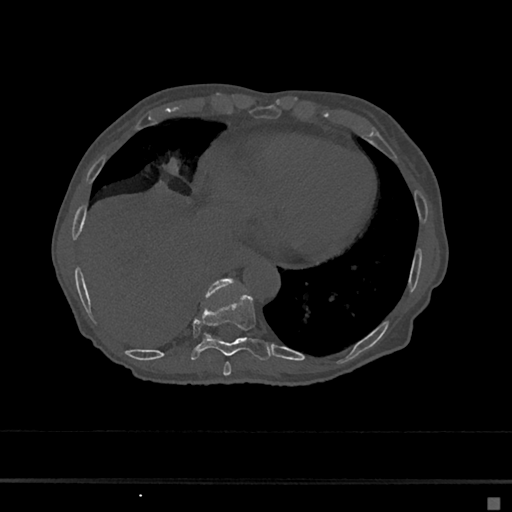
CT including the spine, one axial slice. Position 269 of 797 along the scan axis. 120 kVp. Bone window (W 1800 / L 400 HU). 512 × 512 image matrix, field of view 360 × 360 mm. Patient: female, 68 years. Case-level facts recorded for this patient, not image findings: primary cancer: renal.
Structures marked on this image (semi-automatic segmentation, software-assisted and operator-edited):
- T10 vertebra: box from (x=206, y=279) to (x=233, y=298) px
- T8 vertebra: (x=223, y=362)–(x=232, y=377)
- T9 vertebra: (x=190, y=292)–(x=272, y=360)